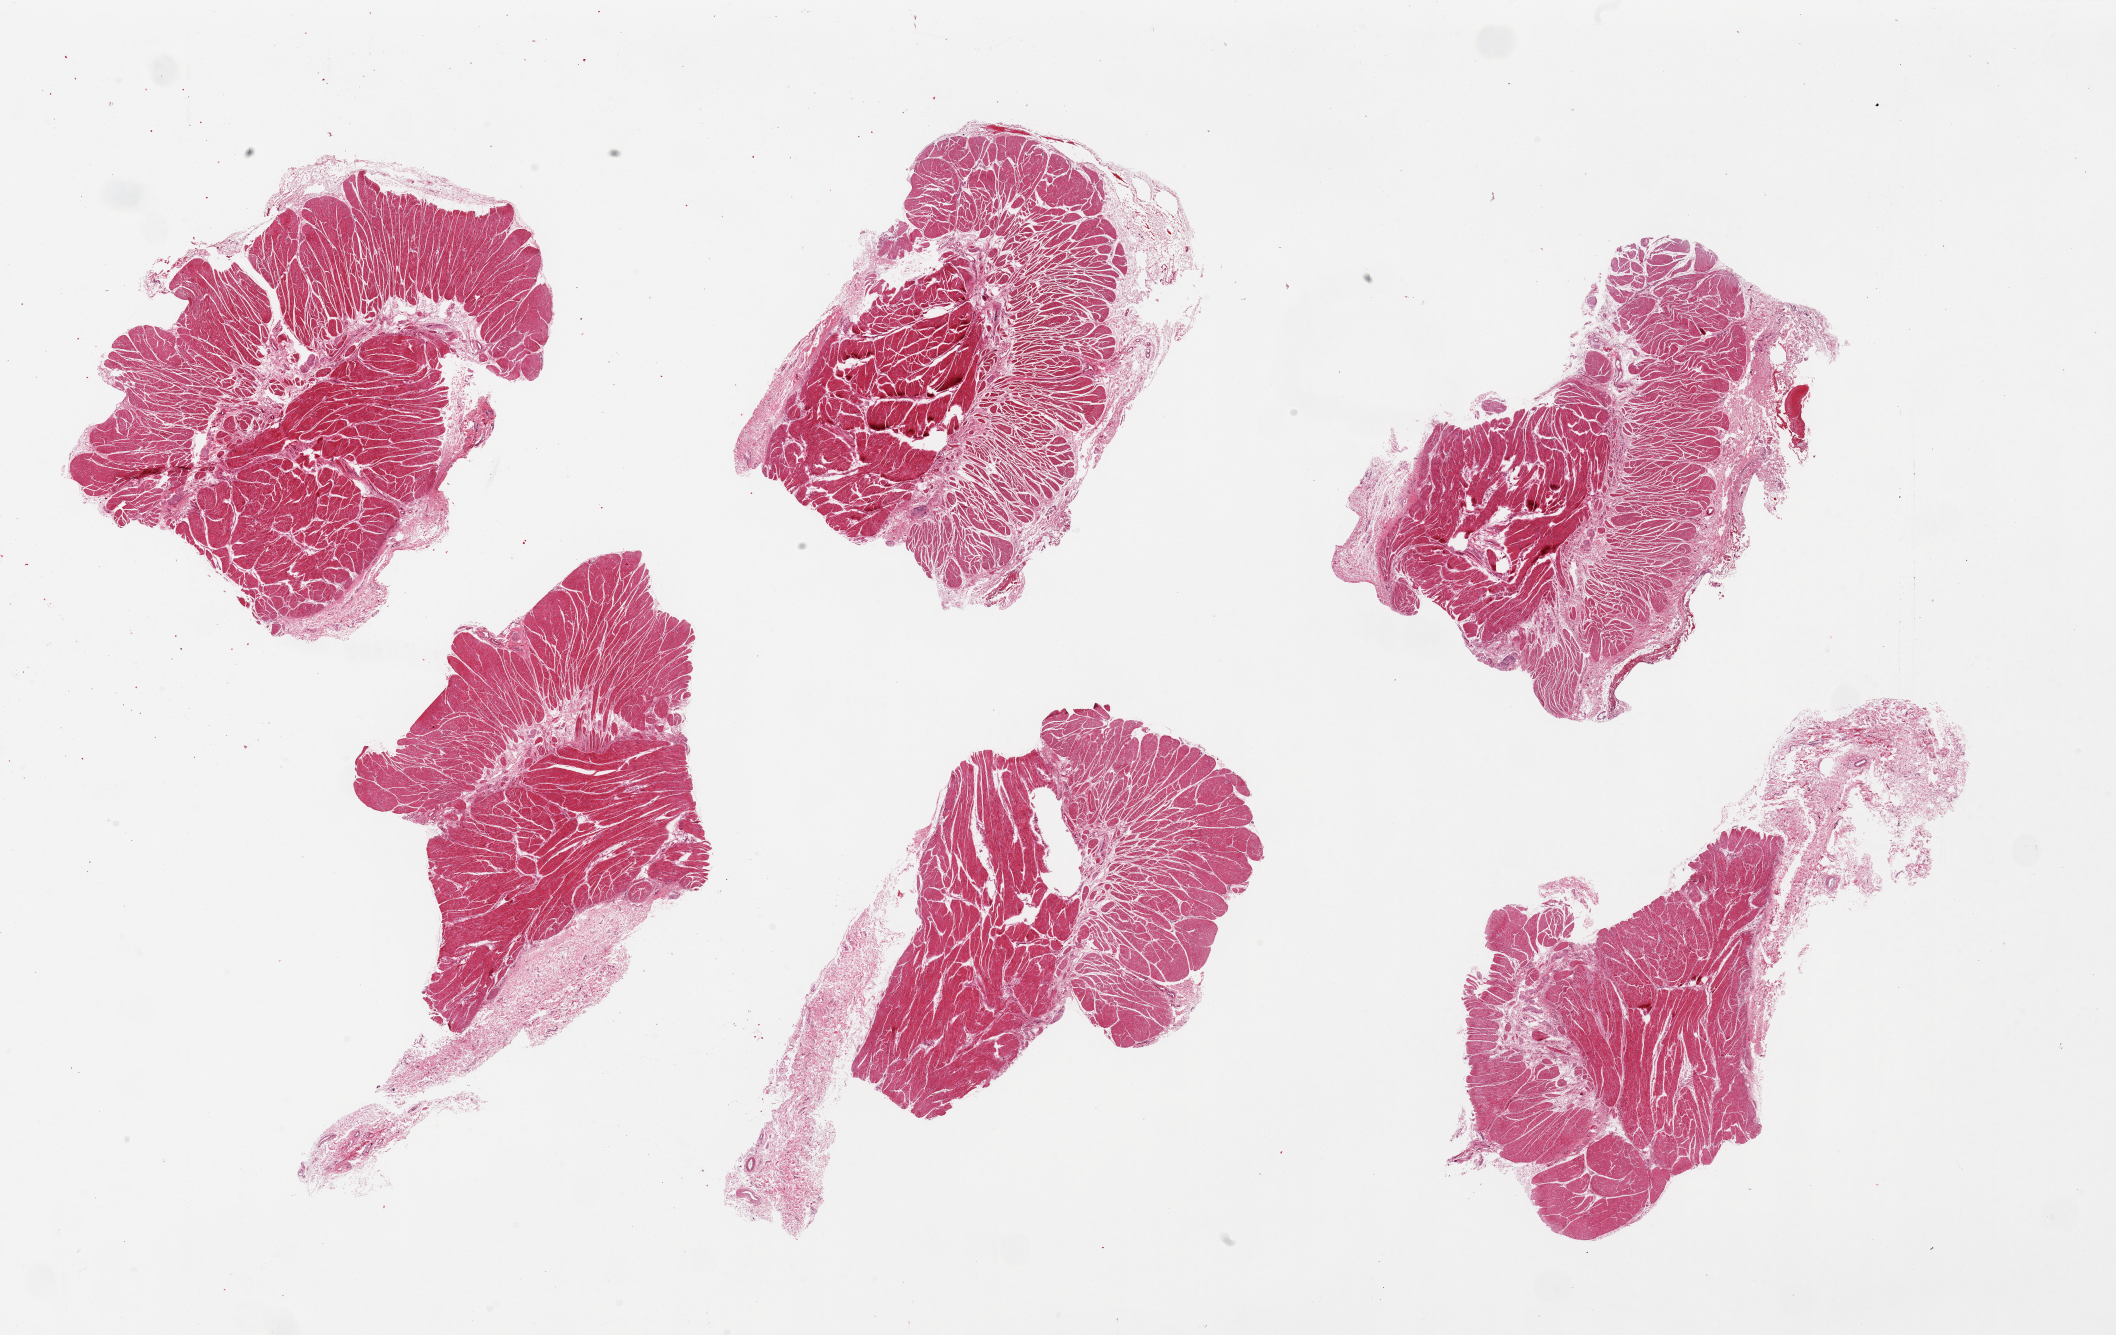
Whole-slide image, H&E stain, shown as a low-resolution overview of the whole scanned area (about 33.5 x 21.1 mm, acquisition: 20x scan); PAXgene-fixed paraffin-embedded (PFPE) section; section of gastroesophageal junction (target tissue); tissue donor sample. Donor sex: female.
Reviewer comment on this tissue sample: 6 pieces, up to 11x6mm; all muscularis, nubbins of attached serosal fibrous tissue up to ~3mm.